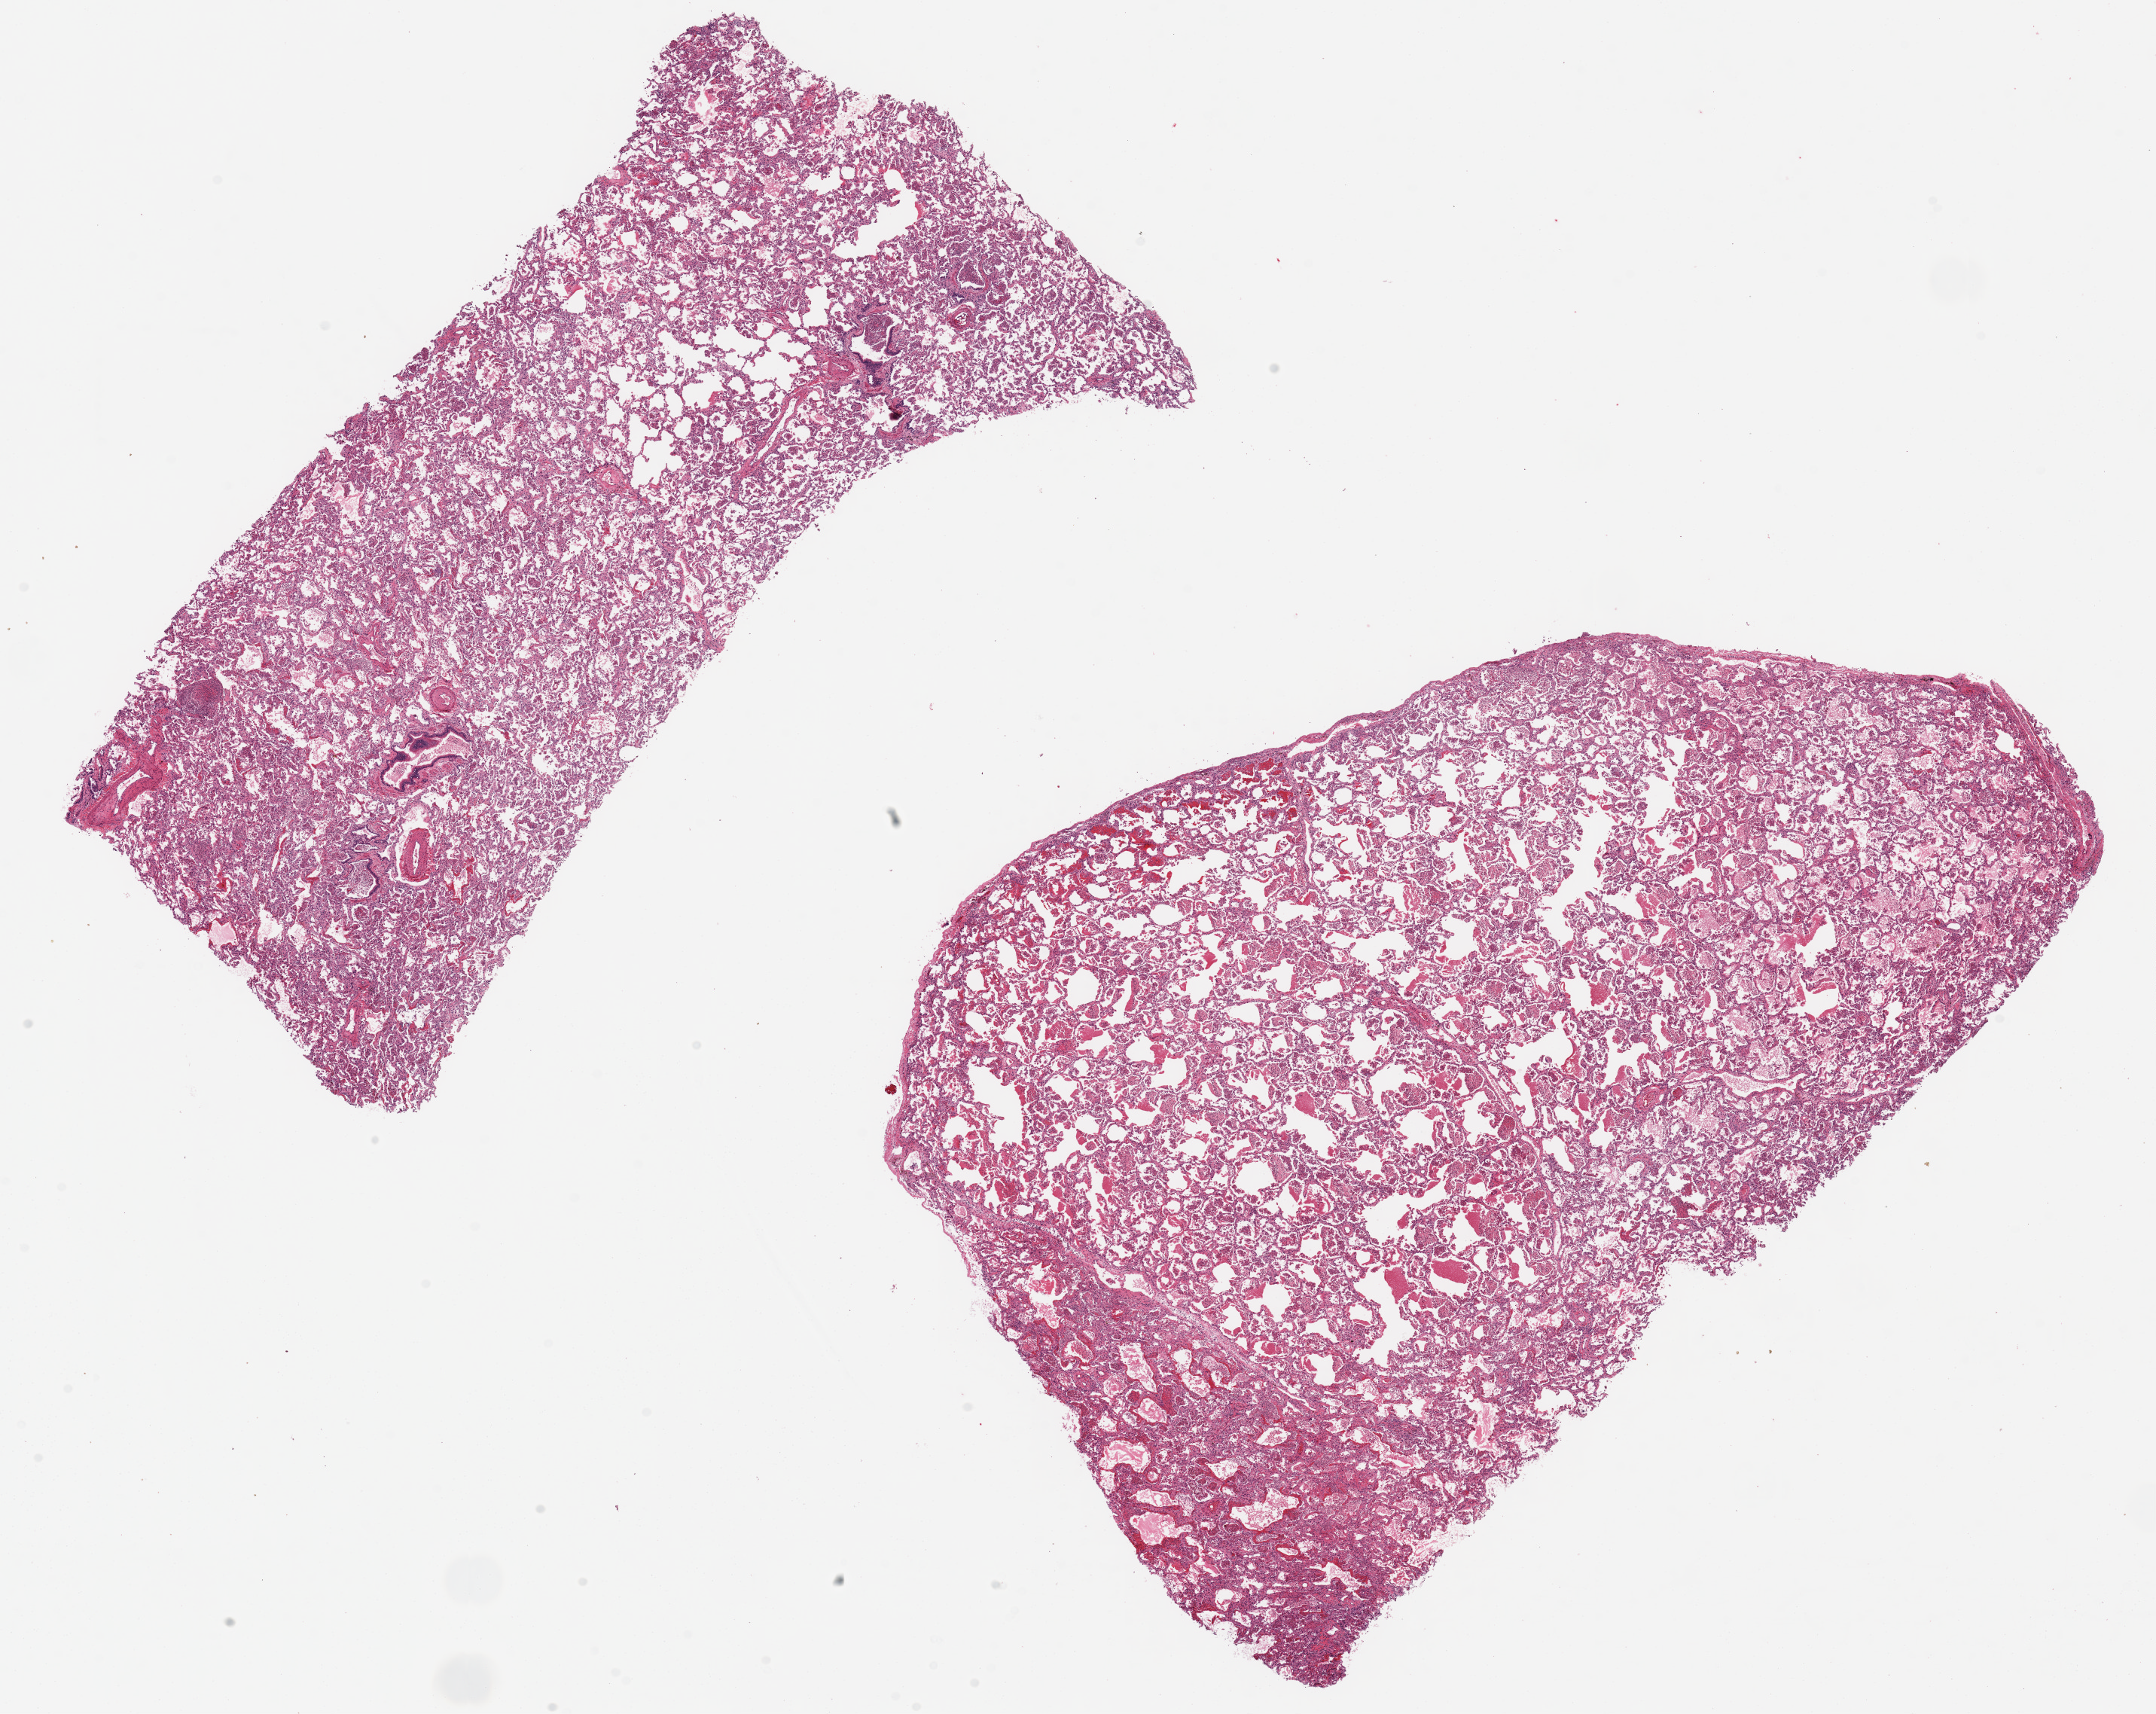
Digitized hematoxylin and eosin (H&E)-stained section, a low-resolution overview of the entire scanned area, about 22.6 x 18.0 mm (acquisition: 20x scan). PAXgene-fixed paraffin-embedded (PFPE) section. Target tissue: lung. Tissue donor sample. Female donor.
• pathologist's review note for this sample: 2 ~11x5mm aliquots. Diffuse mild-moderate acute pneumonitis/edema